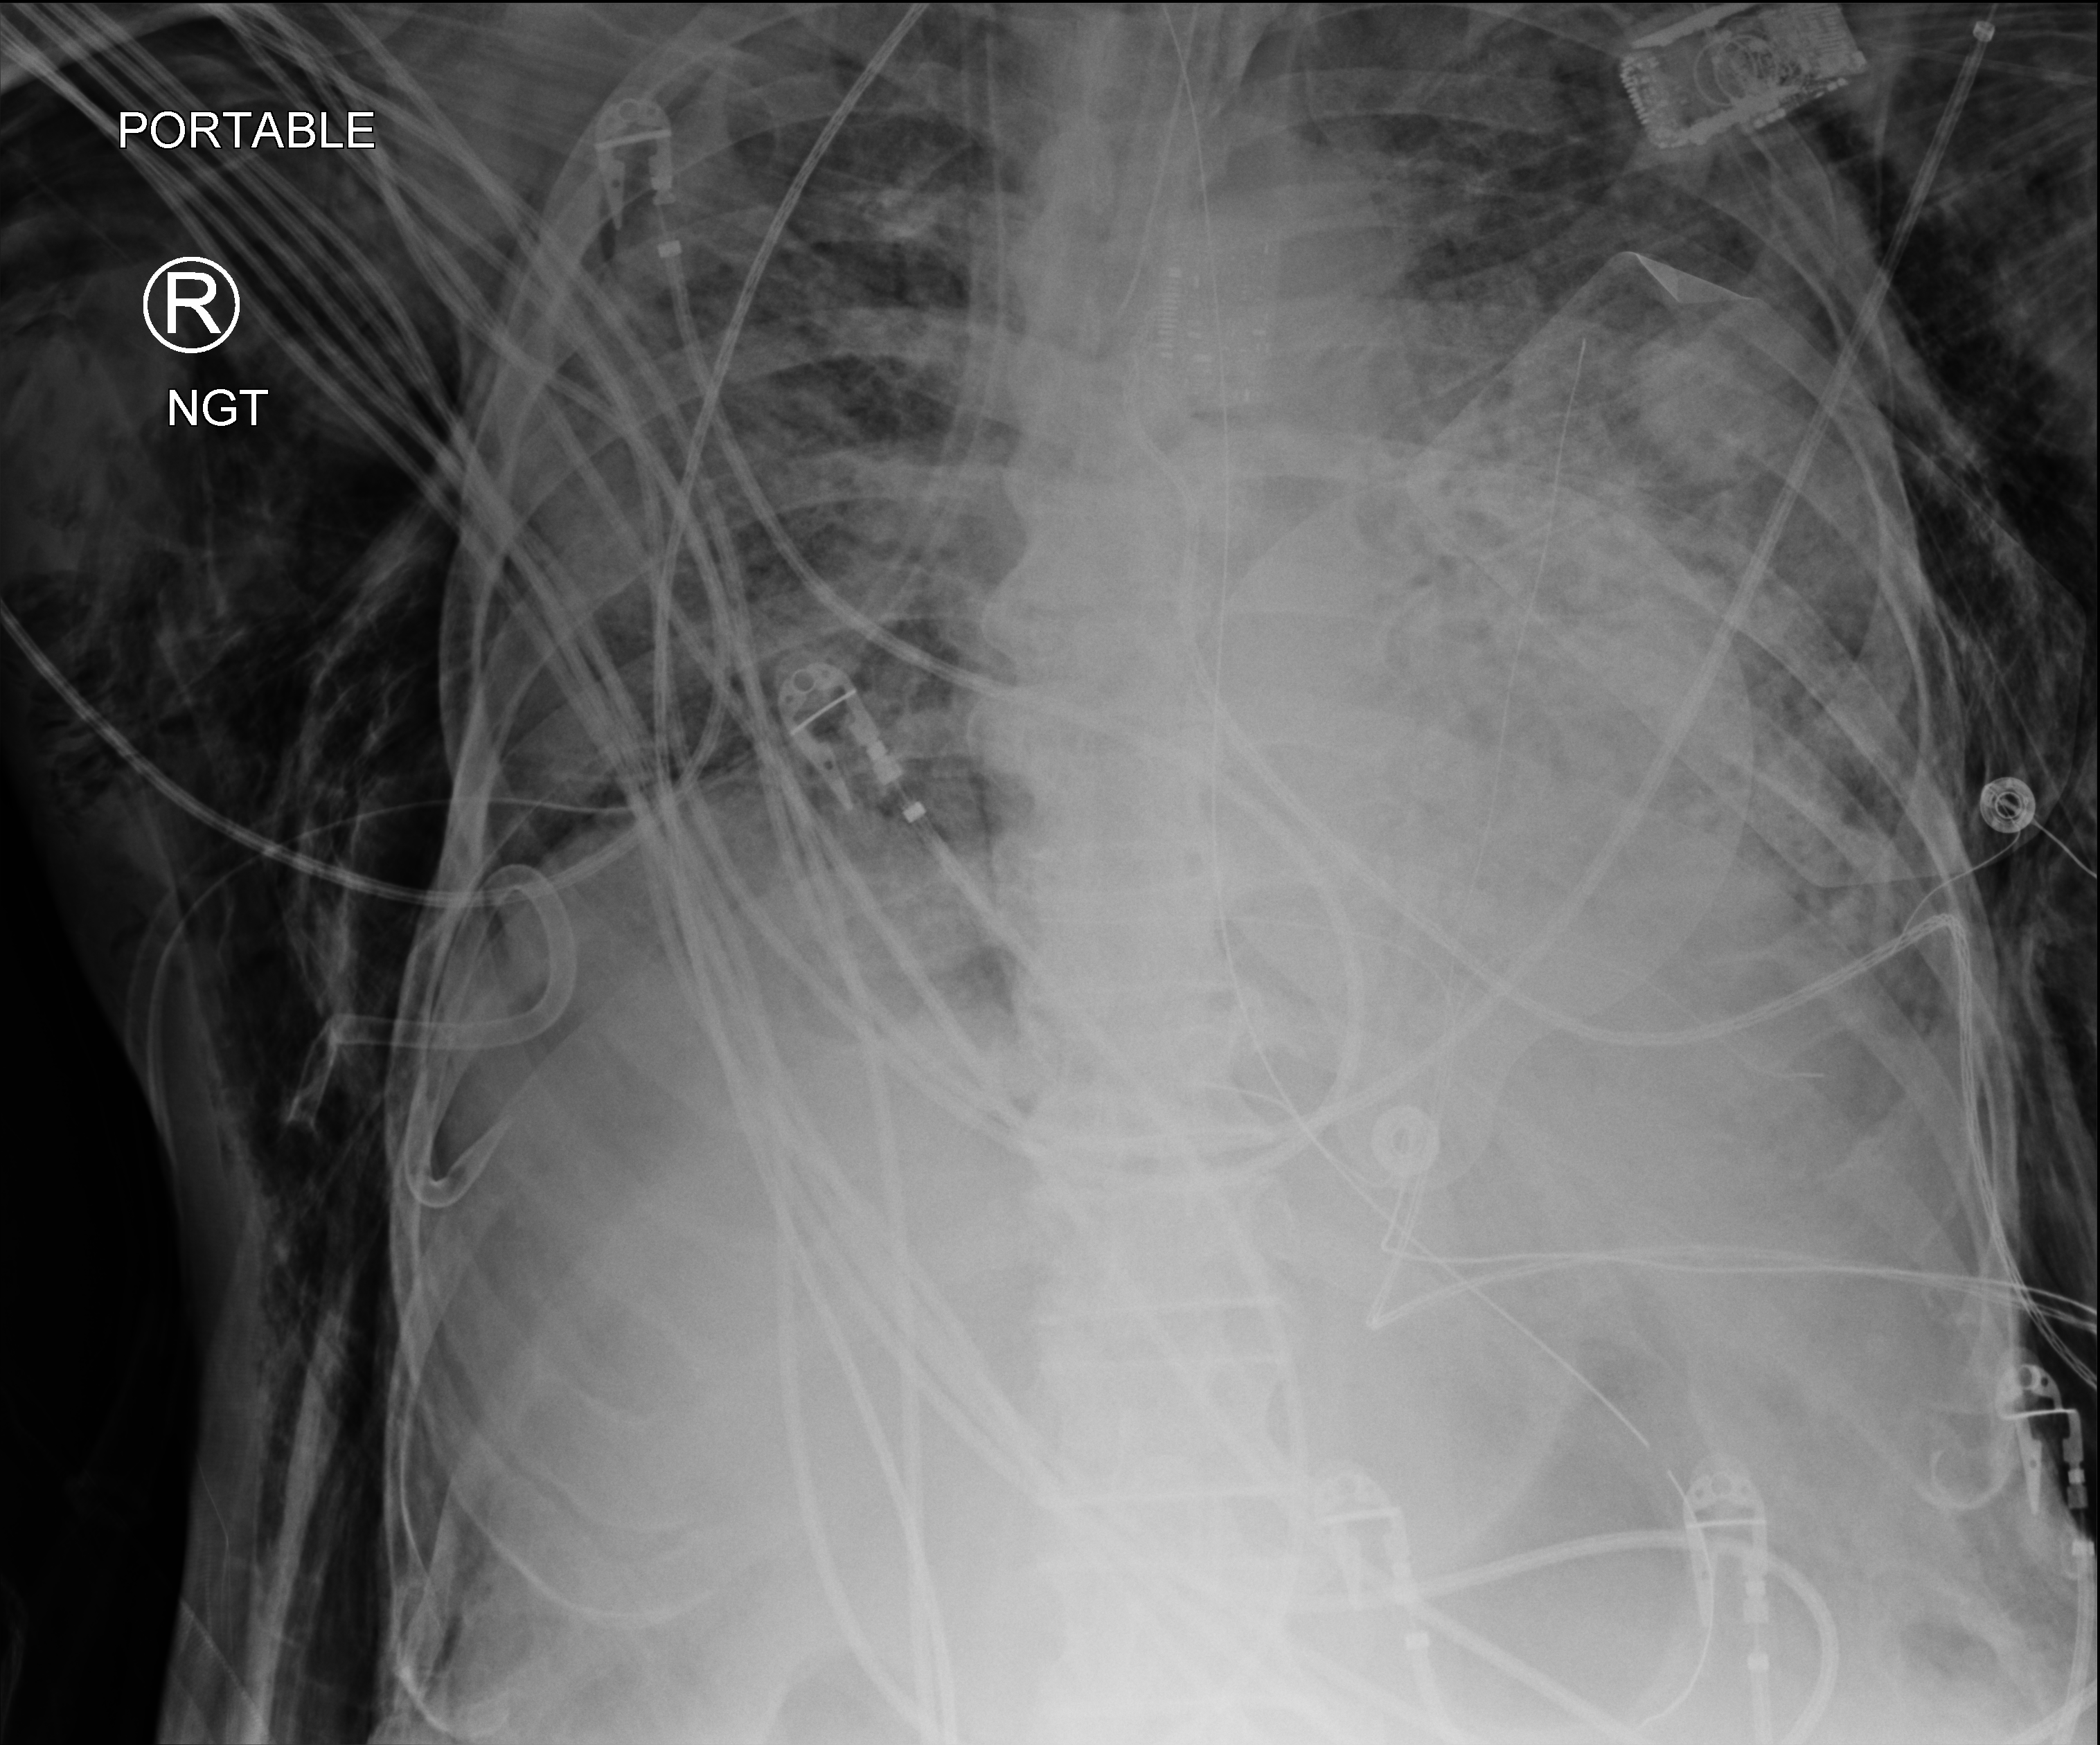
Portable chest radiograph, anteroposterior (AP) projection. Male patient hospitalised with COVID-19, age 75–90 years.
Hospital-stay facts (about this admission, not read from this image; timing relative to this image not recorded):
- mechanically ventilated during this hospital stay: yes
- length of hospital stay: 33 days
- hypertension (admission record): yes